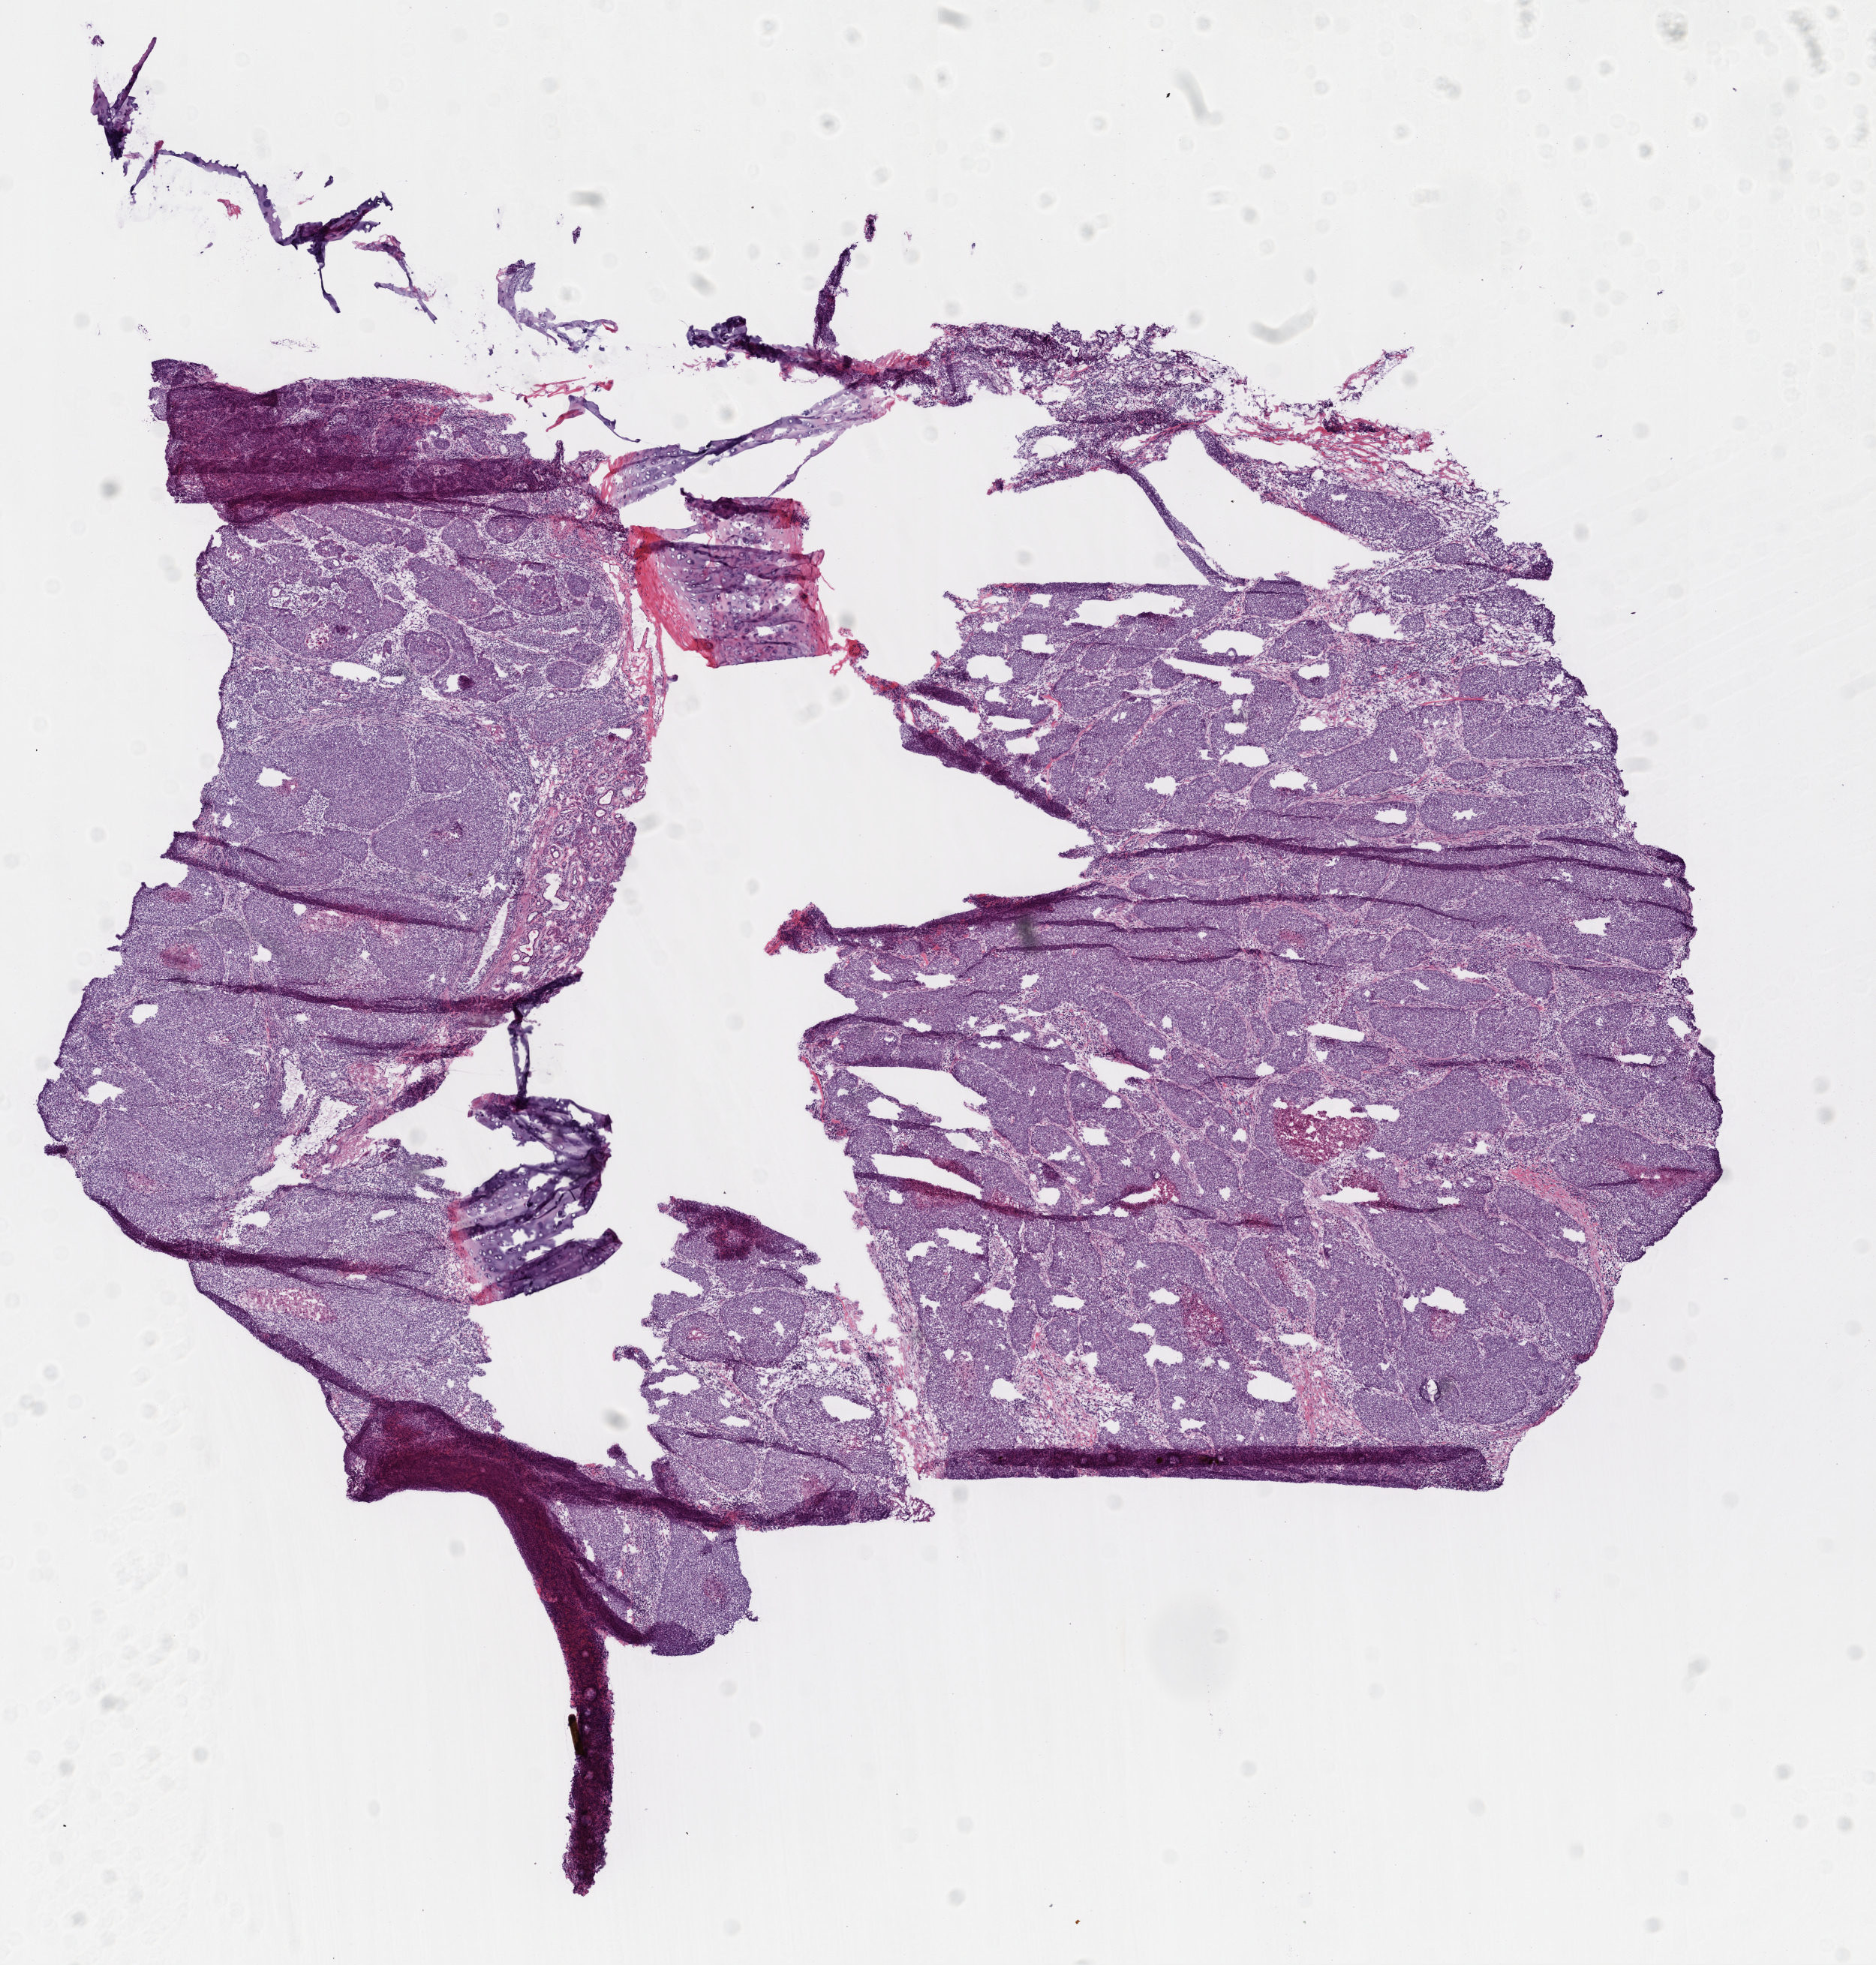
Digitized H&E-stained tissue section (whole slide), a low-resolution overview of the entire scanned area, about 10.0 x 10.5 mm (from a 20x scan). Frozen section from the top of the tissue portion. Sample: primary tumour, lung. Male, age 64 years at initial diagnosis. Pathologist review of this section (percent, as recorded): tumour cells 85%, tumour nuclei 75%, normal cells 5%, stromal cells 5%, necrosis 5%. Infiltration values recorded for this section: lymphocyte infiltration 20%, monocyte infiltration 0%, neutrophil infiltration 0%.
• histologic diagnosis: Squamous cell carcinoma, NOS
• AJCC pathologic stage: IIIB (6th edition)